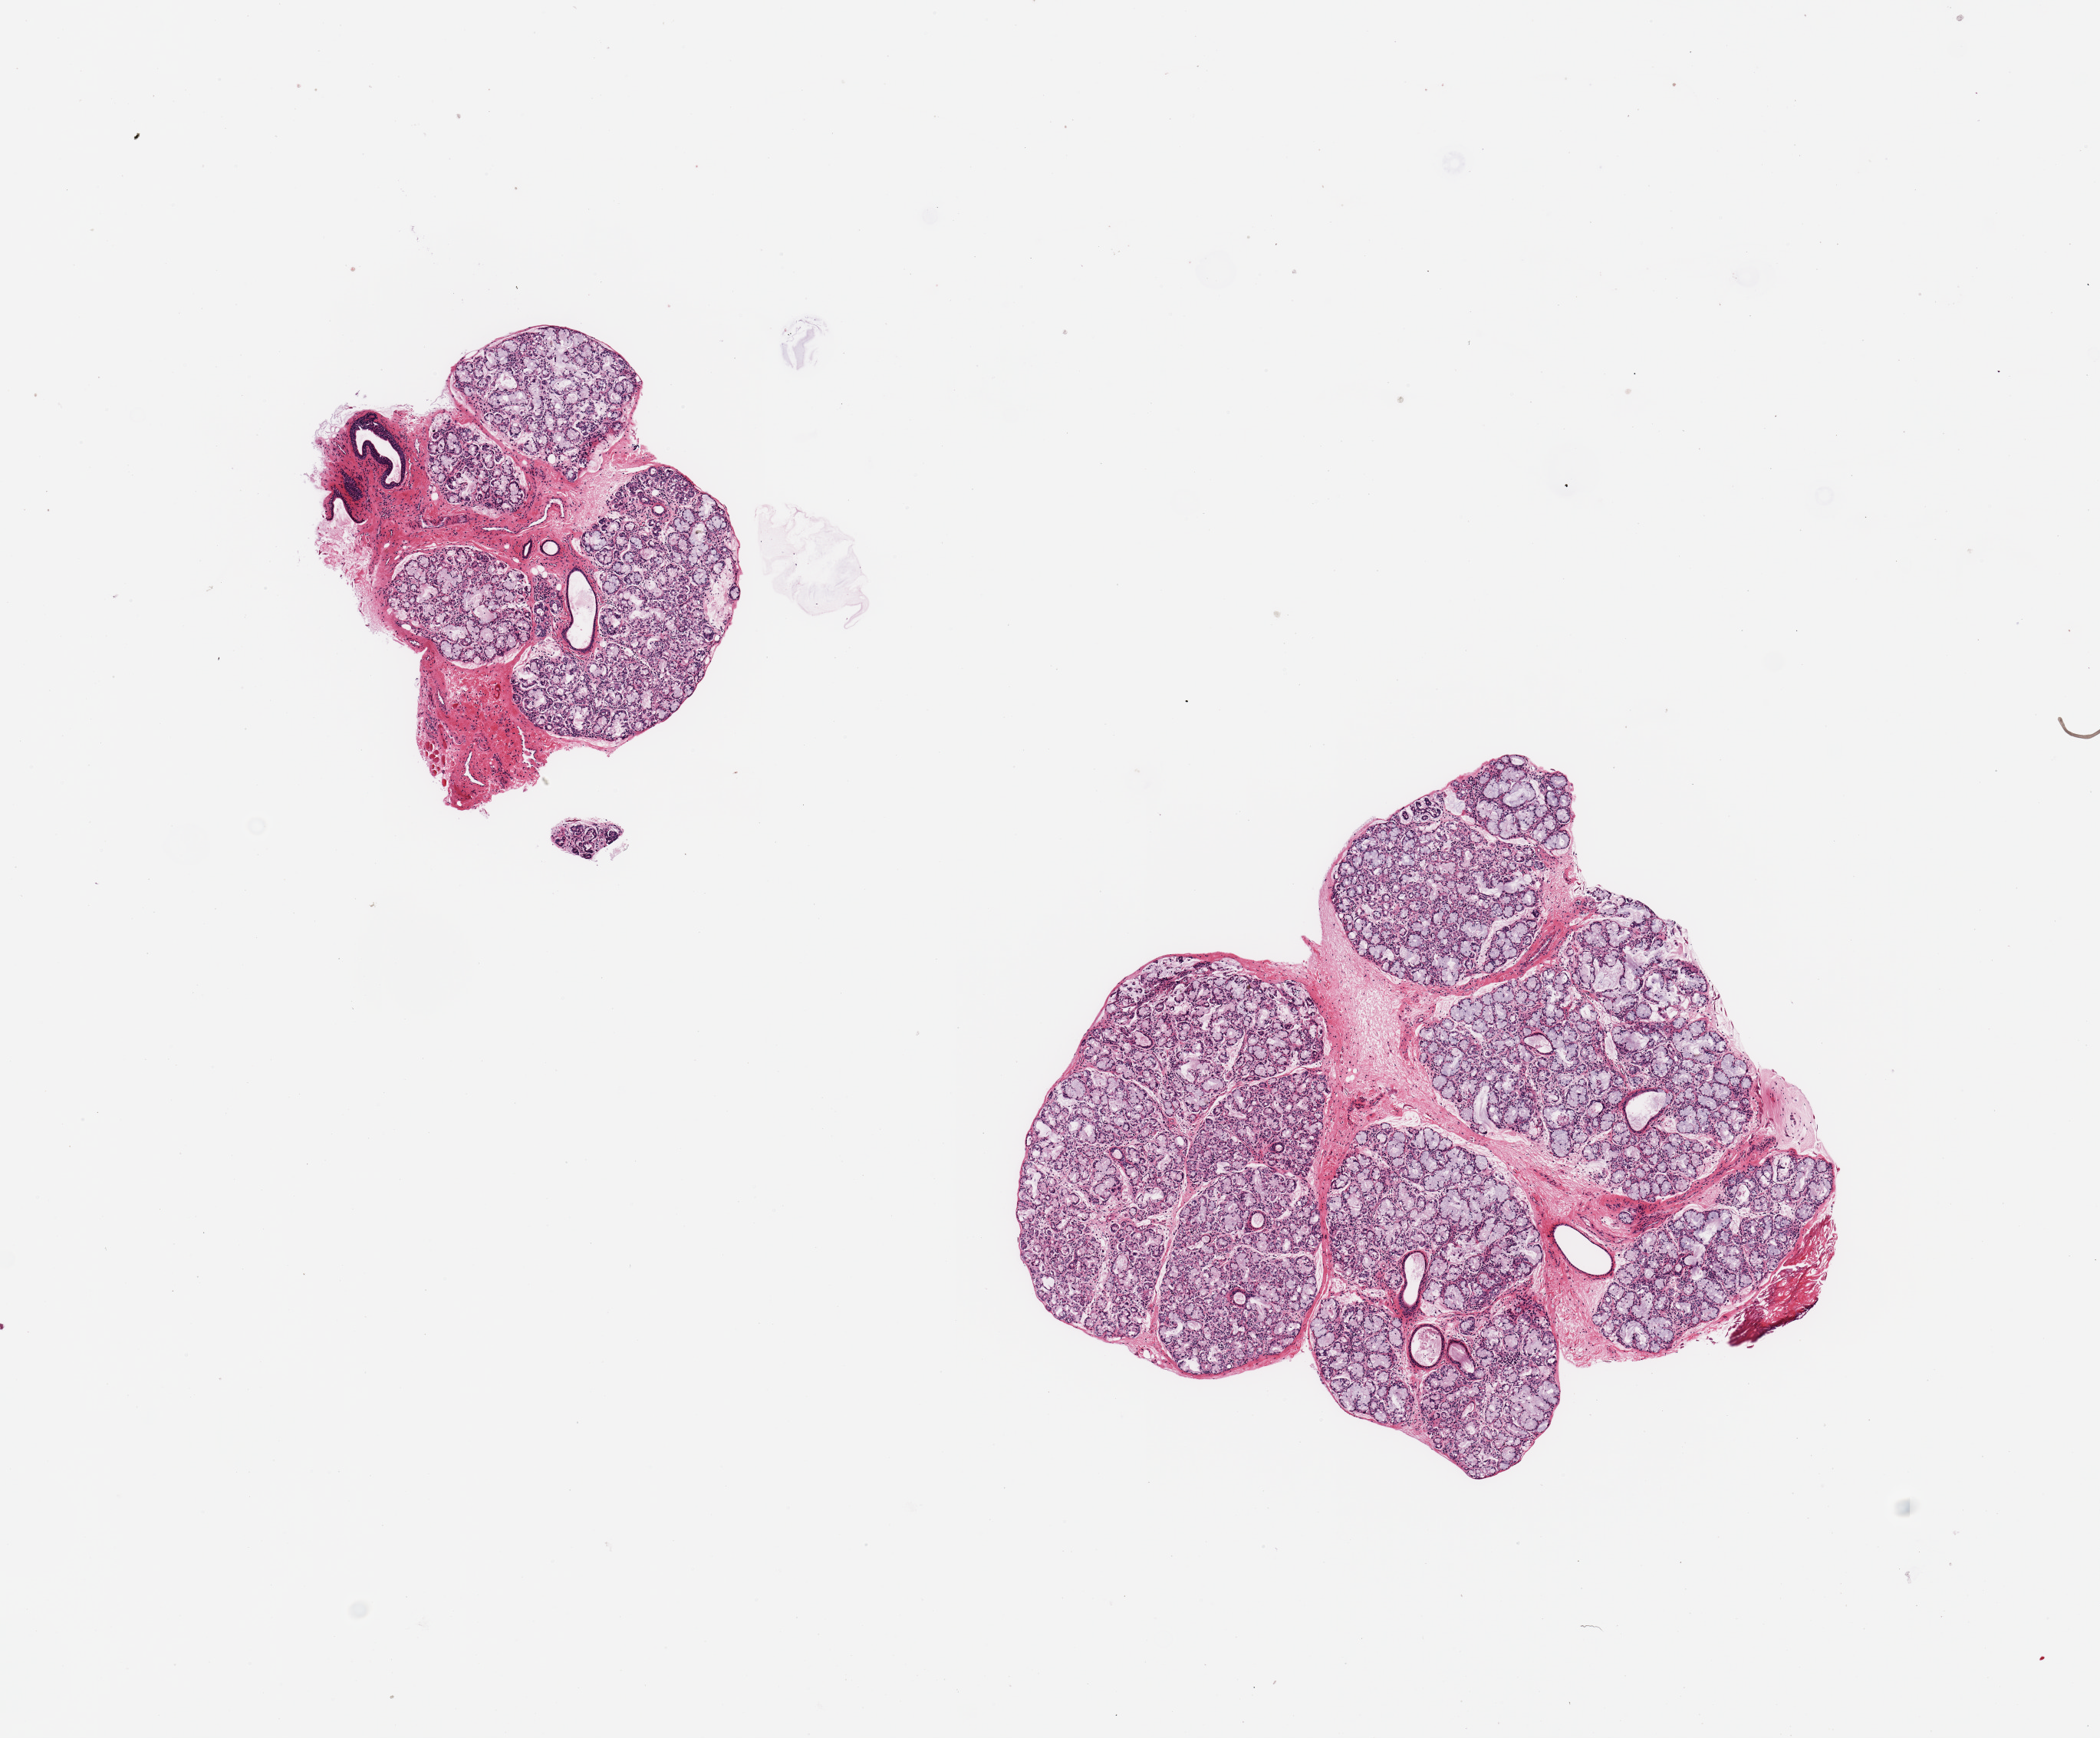
Hematoxylin and eosin (H&E) whole-slide image — low-resolution overview of the scanned area, about 10.8 x 9.0 mm (from a 20x scan), PAXgene-fixed, paraffin-embedded tissue, sampled site (target tissue): minor salivary gland, donor tissue sample.
Review note (as recorded): 2 pieces; well dissected; smaller piece has 40% ducts and stroma; larger piece has 90% glands.